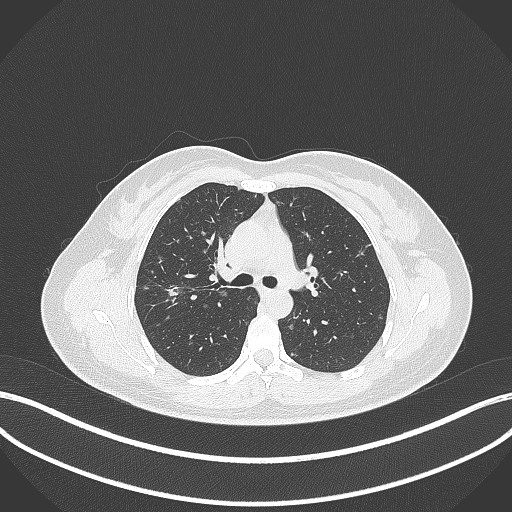
Chest CT, one axial slice. Position 220 of 307 along the scan axis. Lung window (W 1500 / L -600 HU). 512 × 512 image matrix, field of view 400 × 400 mm. Patient: female, 33 years. Case-level facts recorded for this patient, not image findings: clinical TNM (as recorded): T1c N0 M0; histopathological grade: G2-G3.
Structures marked on this image (bounding box drawn by a radiologist):
- lung tumour (recorded histology: adenocarcinoma): bounding box (x1, y1, x2, y2) in pixels: (165, 284, 182, 300)